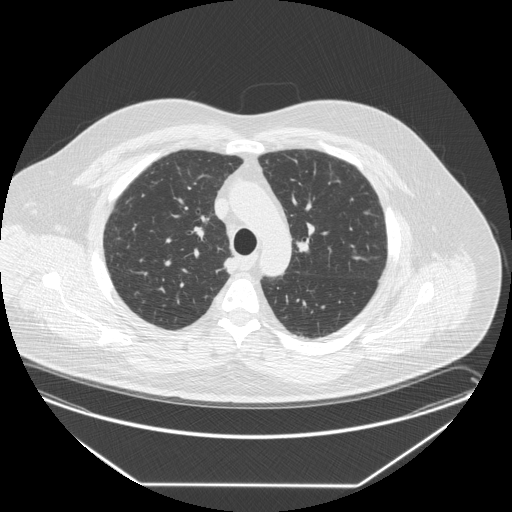
Chest CT (low-dose screening protocol), one axial image, third annual screen, lung window (W 1500 / L -600 HU), 2.5 mm slice thickness, 120 kVp, slice 62 of 258 in the series. Male participant, aged 58 years at enrolment. Former smoker at enrolment.
Expert reader's lesion annotation, bounding box <212,253,242,277> (left, top, right, bottom; pixels). The exam's reader record, not a measurement of the box and not confirmed to be the same lesion: non-calcified nodule or mass ≥4 mm, right upper lobe, 15 × 12 mm, smooth margins, soft tissue attenuation, pre-existing on the prior screen: no. Official screen result: positive, other.